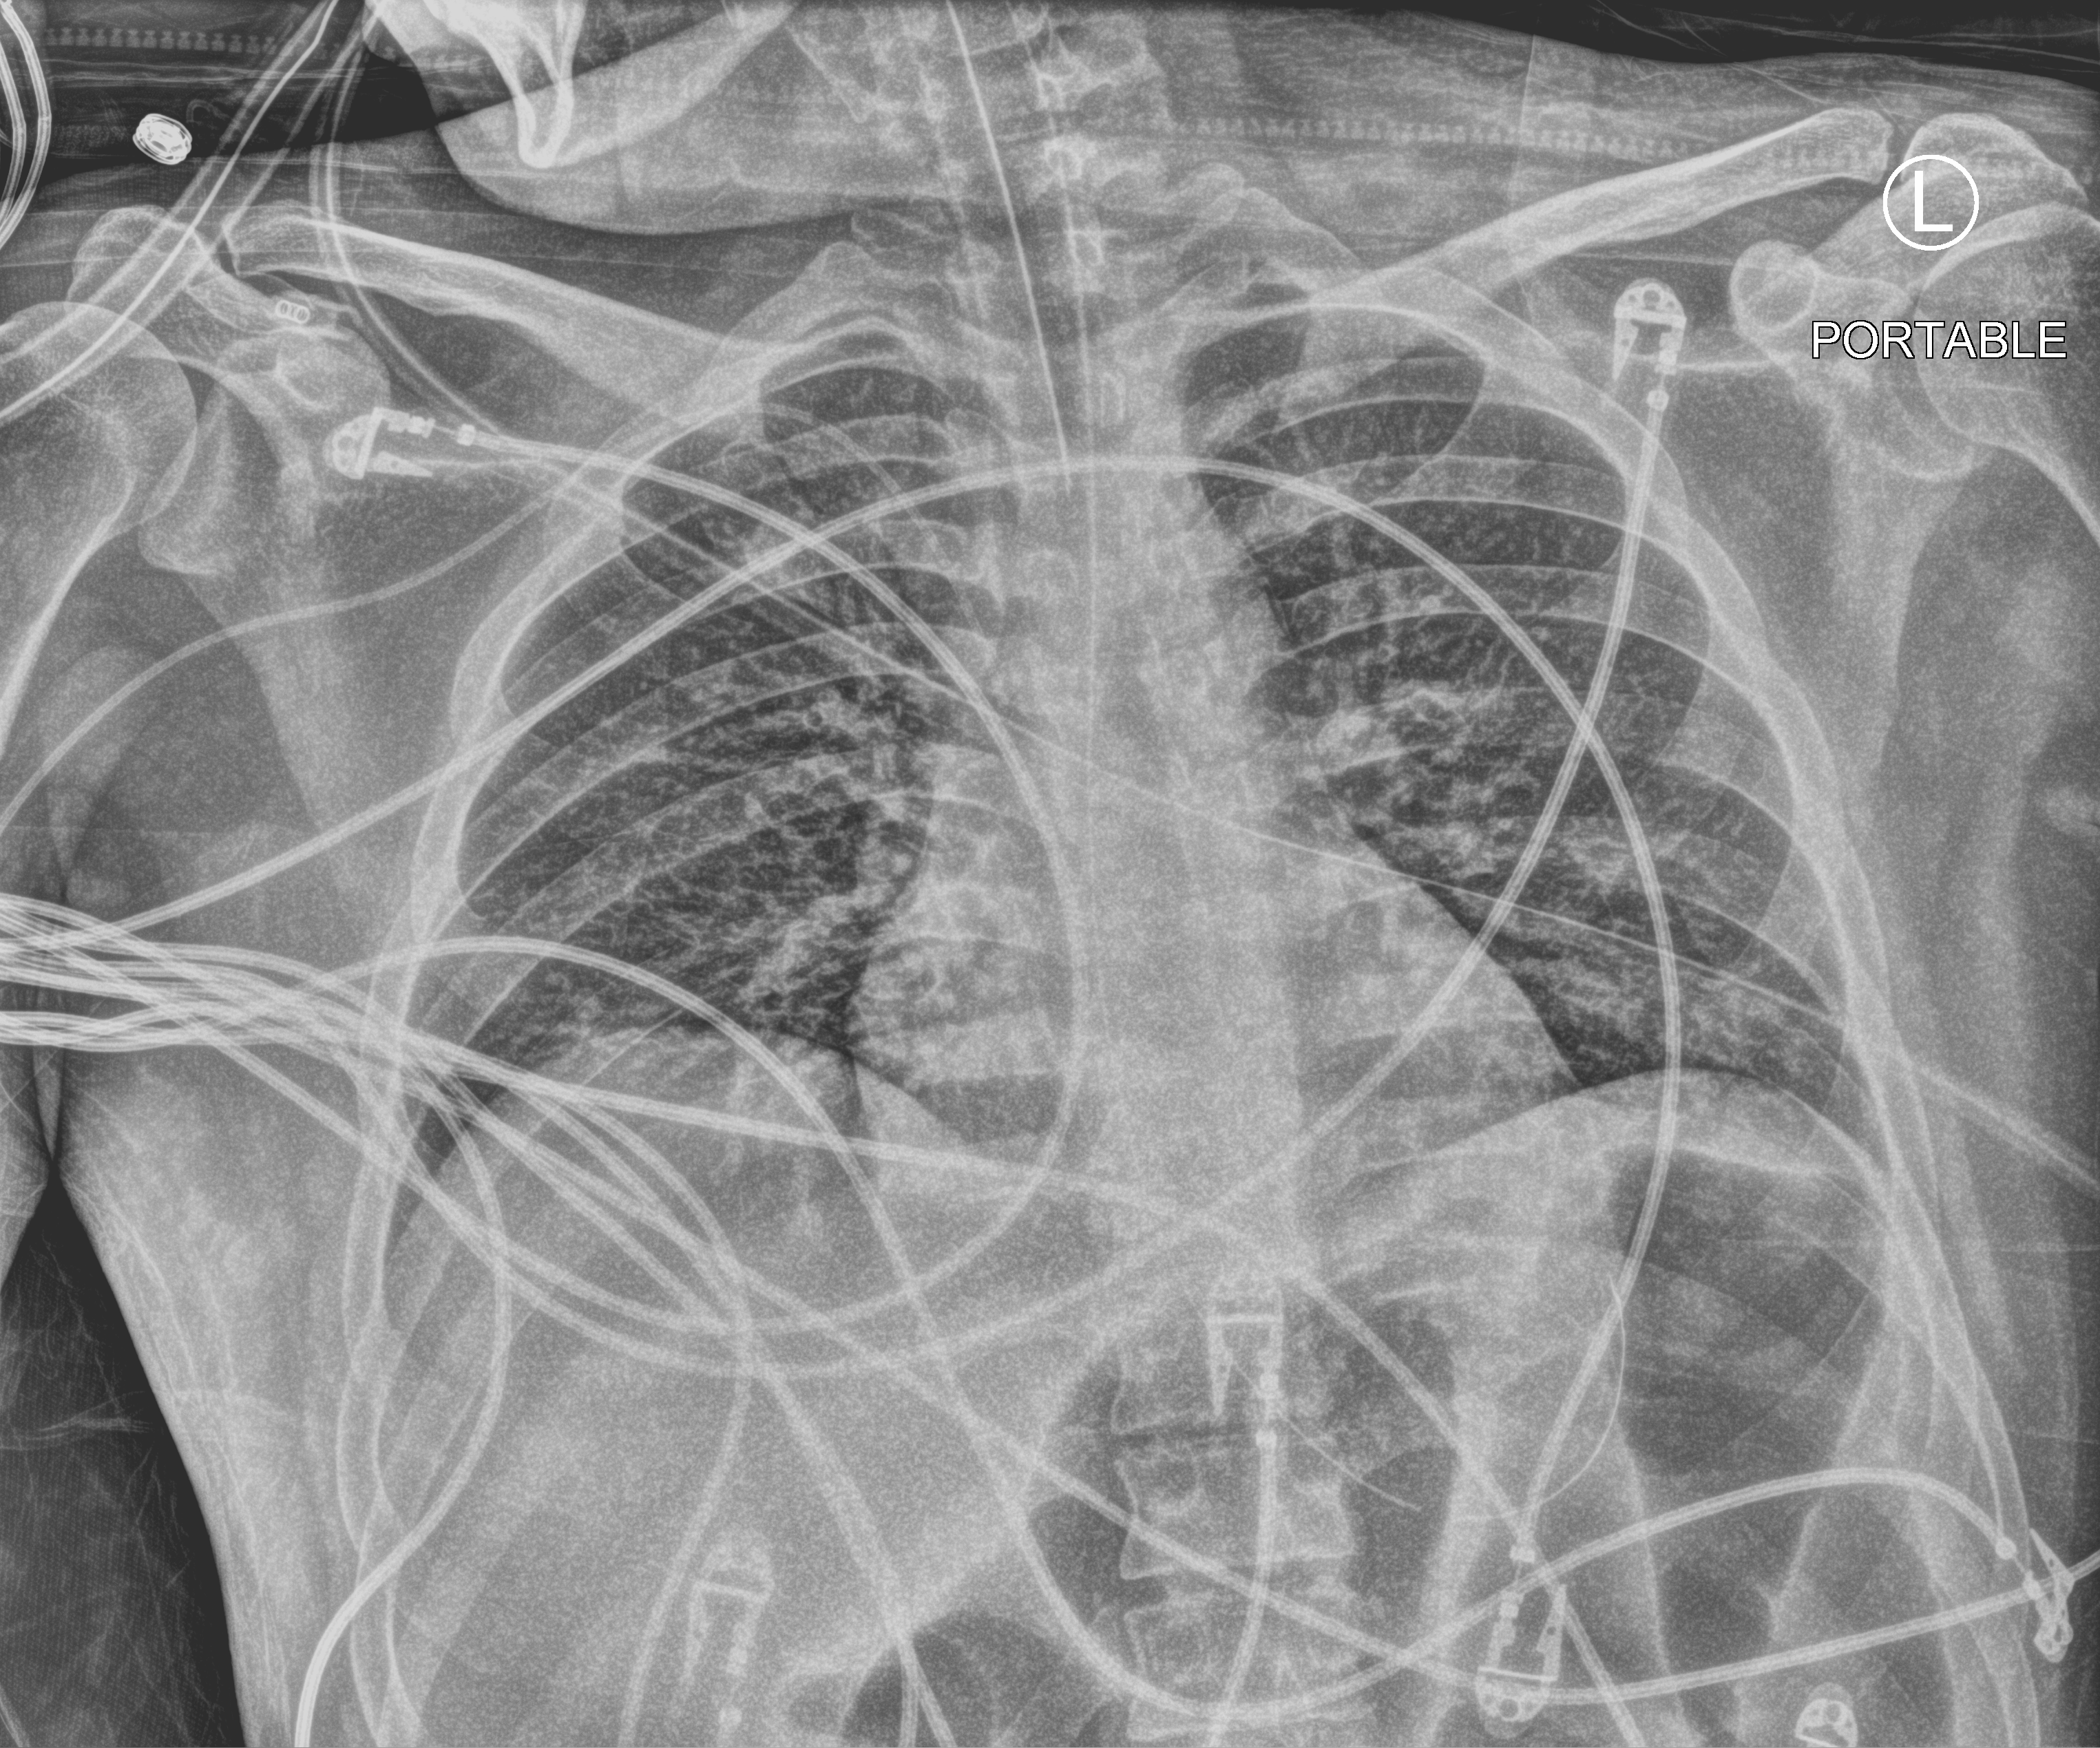
Portable chest radiograph. Patient hospitalised with COVID-19; male, aged 18–59 years.
From the hospital-stay record, not from the radiograph (when in the stay this image was taken is not recorded):
- smoking status (admission record): former
- length of hospital stay: 44 days
- admitted to intensive care during this hospital stay: yes